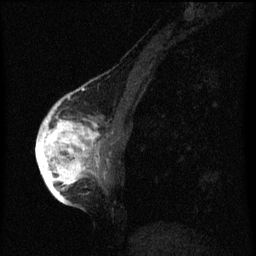
Breast MRI (dynamic contrast-enhanced), one sagittal slice; slice 24 of 60 in the series (ordered by position); dynamic contrast-enhanced series, image 2 of 3 at this slice position (ordered by acquisition); 1.5 T; TE 4.2 ms, TR 8 ms; 256 × 256 image matrix, field of view 180 × 180 mm. Female patient, age 56 years.
Outlined on this slice (semi-automatically segmented with operator editing):
- analysis volume of interest (the breast-tissue region the enhancement analysis was run in; not a lesion): bounding box (x1, y1, x2, y2) in pixels: (42, 110, 103, 193)
- tumour enhancement mask (voxels above the 70 % enhancement threshold inside the analysis volume of interest): (42, 110, 101, 193)